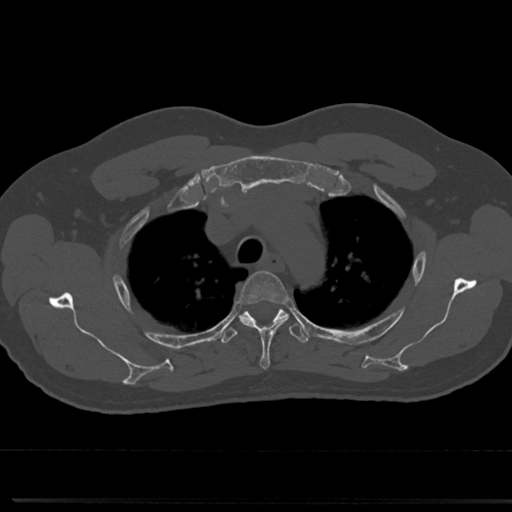
CT including the spine, one axial slice. Position 572 of 817 along the scan axis. Reconstruction kernel Br40s/3. 120 kVp. Bone window (W 1800 / L 400 HU). 0.5 mm slice thickness. 512 × 512 image matrix. Male patient, age 61 years. Case-level facts recorded for this patient, not image findings: primary cancer: prostate.
Structures marked on this image (semi-automatic segmentation, software-assisted and operator-edited):
- T3 vertebra: bounding box <241,270,285,369> (left, top, right, bottom; pixels)
- T4 vertebra: <219,301,310,345>